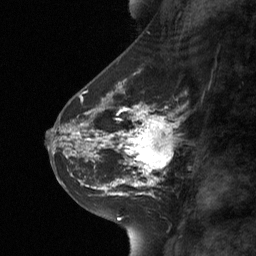
Breast MRI (dynamic contrast-enhanced), one sagittal slice; position 28 of 64 along the scan axis; dynamic contrast-enhanced study with each time point stored as its own series, time point 2 of 3 at this slice position (early post-contrast, ordered by acquisition time); 1.5 T; TE 4.8 ms, TR 27 ms; 2 mm slice thickness; 256 × 256 image matrix. Female patient, age 42 years. Case-level facts recorded for this patient, not image findings: setting: breast cancer imaged before/during neoadjuvant chemotherapy; receptor status: triple-negative.
Structures marked on this image (semi-automatically segmented with operator editing):
- analysis volume of interest (the breast-tissue region the enhancement analysis was run in; not a lesion): bounding box [x1, y1, x2, y2] px = [111, 104, 186, 178]
- tumour enhancement mask (voxels above the 90 % enhancement threshold inside the analysis volume of interest): [118, 109, 172, 178]